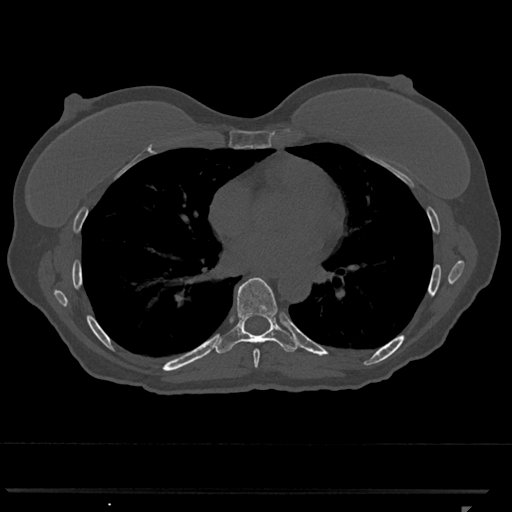
CT including the spine, one axial slice; slice 675 of 793 in the series (ordered by position); 120 kVp; bone window (W 1800 / L 400 HU); 512 × 512 image matrix, field of view 380 × 380 mm. Patient: female, 62 years. From the clinical record (not read from this slice): primary cancer: renal.
Outlined on this slice (semi-automatic segmentation, software-assisted and operator-edited):
- T7 vertebra: bounding box <253,349,260,368> (left, top, right, bottom; pixels)
- T8 vertebra: <214,277,299,354>